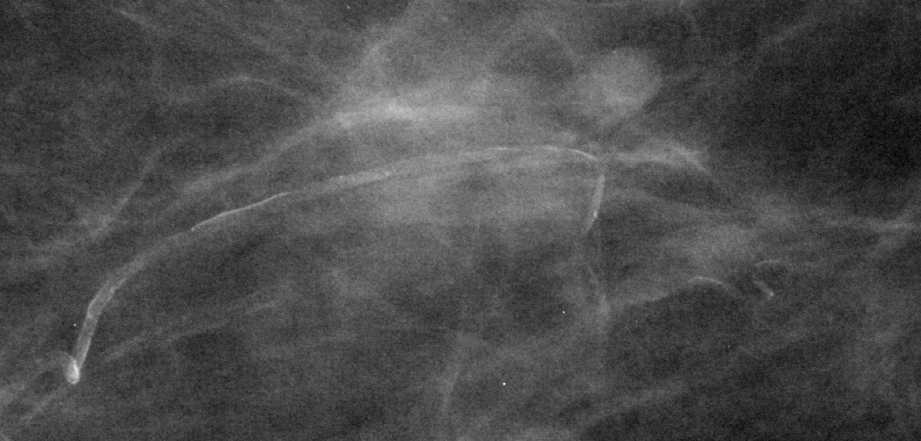
Region of interest cut from a scanned film mammogram (one marked finding); left breast; CC view.
Calcifications, morphology vascular; BI-RADS assessment category 2; benign without callback (not worked up further).